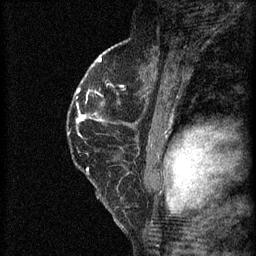
Breast MRI (dynamic contrast-enhanced), one sagittal slice. Slice 39 of 60 in the series (ordered by position). 3 images stored at this slice position (order not interpretable as contrast timing). 1.5 T. TE 4.2 ms, TR 8.2 ms. 256 × 256 image matrix, field of view 180 × 180 mm. Patient: female, 45 years.
Structures marked on this image (semi-automatic segmentation, software-assisted and operator-edited):
- analysis volume of interest (the breast-tissue region the enhancement analysis was run in; not a lesion): box from (x=68, y=104) to (x=104, y=137) px
- tumour enhancement mask (voxels above the 70 % enhancement threshold inside the analysis volume of interest): (x=77, y=120)–(x=83, y=121)